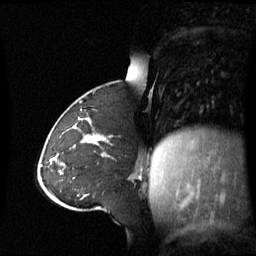
Breast MRI (dynamic contrast-enhanced), one sagittal slice. Slice 25 of 60 in the series (ordered by position). Dynamic contrast-enhanced series, image 2 of 3 at this slice position (ordered by acquisition). 1.5 T. TE 4.2 ms, TR 8.4 ms. 256 × 256 image matrix, field of view 270 × 270 mm. Female patient, age 43 years. Case-level facts recorded for this patient, not image findings: setting: breast cancer imaged before/during neoadjuvant chemotherapy; receptor status: triple-negative.
Annotated regions visible in this slice (semi-automatically segmented with operator editing):
- analysis volume of interest (the breast-tissue region the enhancement analysis was run in; not a lesion): bounding box <55,124,109,173> (left, top, right, bottom; pixels)
- tumour enhancement mask (voxels above the 70 % enhancement threshold inside the analysis volume of interest): <73,125,104,143>